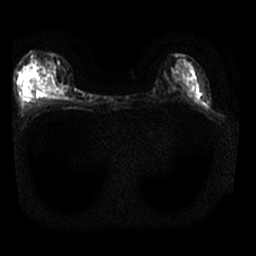
Breast MRI, one axial slice; slice 15 of 25 in the series (ordered by position); diffusion-weighted series; image 2 of 4 stored at this slice position (different b-values; order by instance number); 1.5 T; 4 mm slice thickness; 256 × 256 image matrix, field of view 310 × 310 mm. Female patient.
Outlined on this slice (outlined manually by an expert reader):
- tumour on diffusion-weighted imaging: bounding box [x1, y1, x2, y2] px = [38, 83, 54, 89]